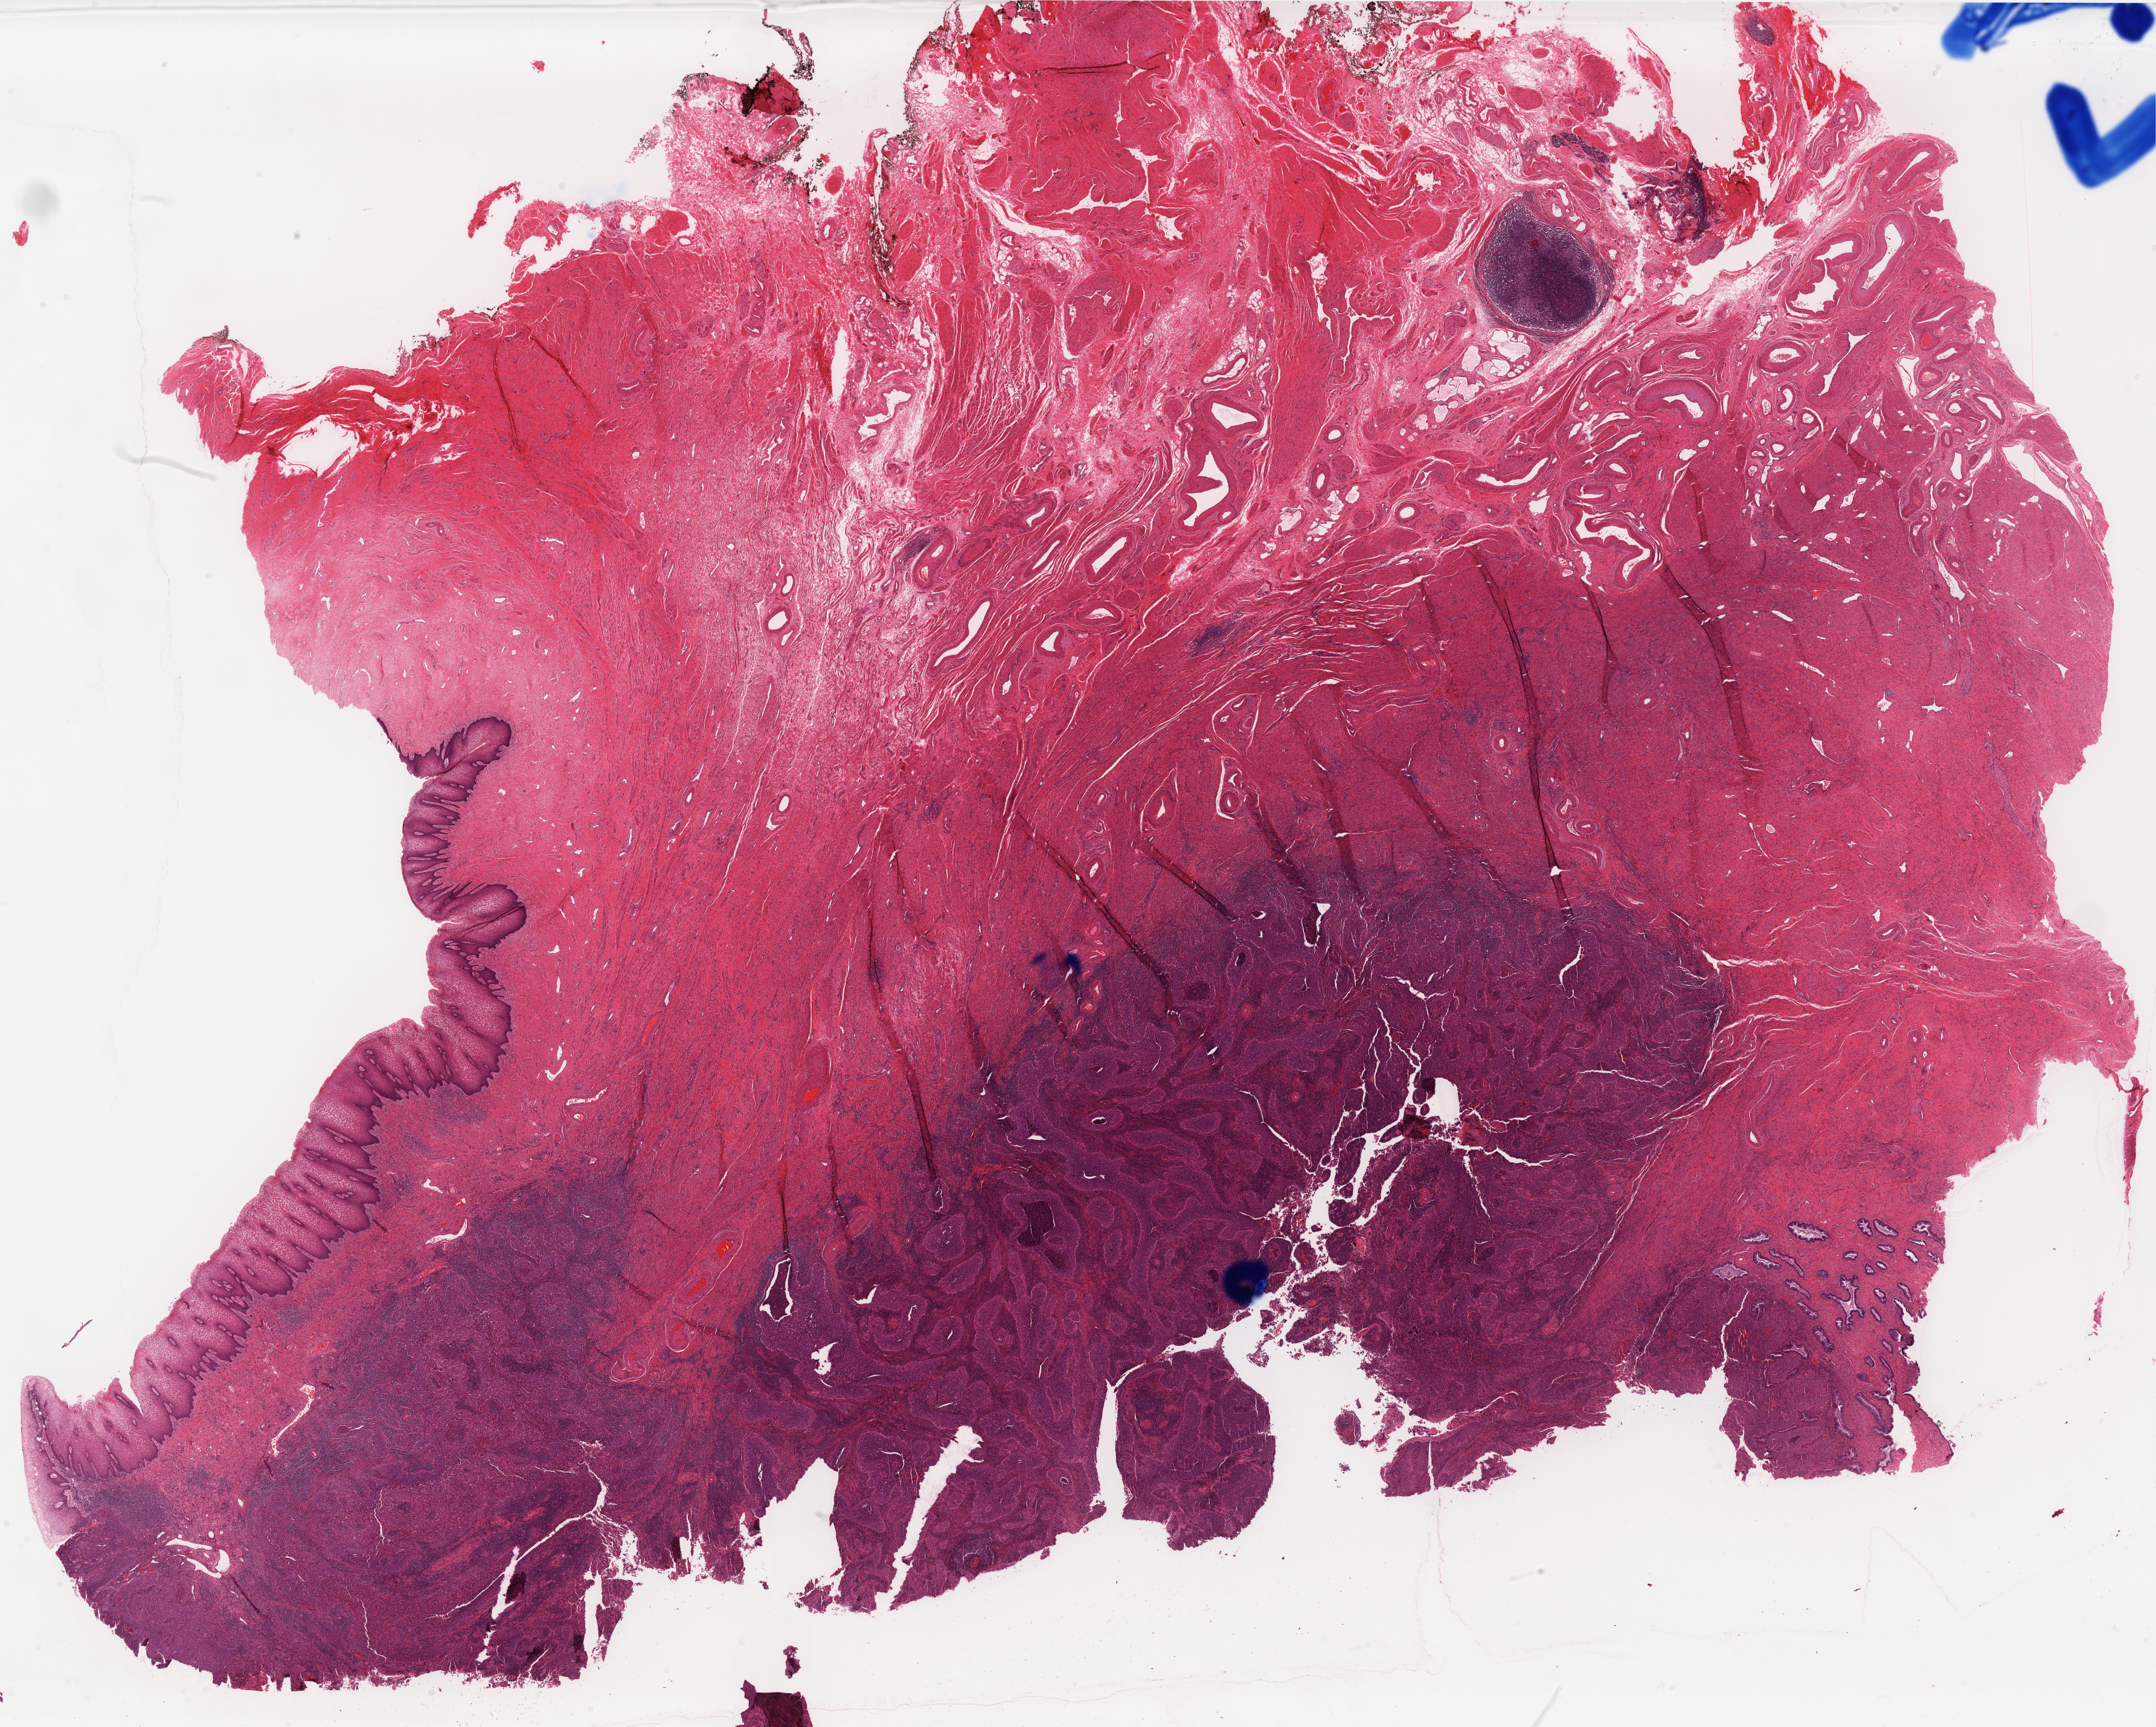
H&E whole-slide image — shown as a low-resolution overview of the whole scanned area (about 28.6 x 22.9 mm); formalin-fixed paraffin-embedded (FFPE) diagnostic section; sample: primary tumour, cervix. Female, age 37 years at initial diagnosis. Histologic grade: G2 (moderately differentiated).
Lymph nodes positive (case pathology): 0 of 30 examined. FIGO stage: IB. Histologic diagnosis: Squamous cell carcinoma, NOS (cervix uteri).